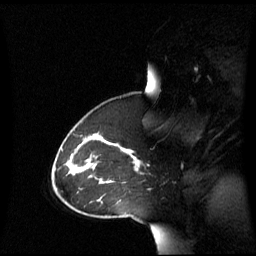
Breast MRI (dynamic contrast-enhanced), one sagittal slice; position 42 of 60 along the scan axis; dynamic contrast-enhanced series, image 2 of 3 at this slice position (ordered by acquisition); 1.5 T; TE 4.2 ms, TR 8.4 ms; 2.8 mm slice thickness; 256 × 256 image matrix, field of view 270 × 270 mm. Female patient, age 43 years. Case-level facts recorded for this patient, not image findings: setting: breast cancer imaged before/during neoadjuvant chemotherapy; receptor status: triple-negative.
Annotated regions visible in this slice (semi-automatically segmented with operator editing):
- analysis volume of interest (the breast-tissue region the enhancement analysis was run in; not a lesion): box from (x=69, y=137) to (x=141, y=198) px
- tumour enhancement mask (voxels above the 70 % enhancement threshold inside the analysis volume of interest): (x=120, y=147)–(x=140, y=168)